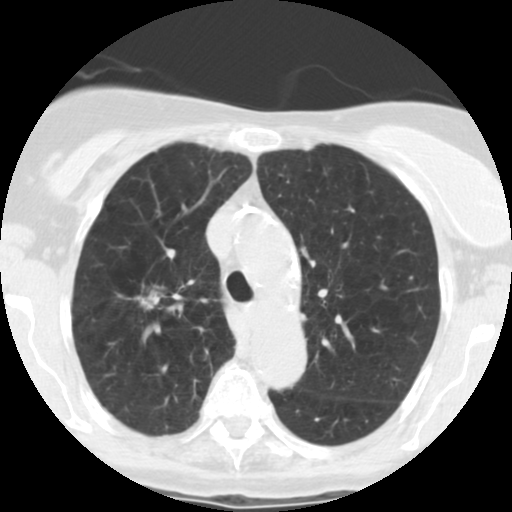
Axial slice from a low-dose chest CT screening exam, first (baseline) screen, lung window (W 1500 / L -600 HU), 2.5 mm slice thickness, slice 181 of 246 in the series. Female participant, aged 67 years at enrolment.
• Lesion marked by an expert reader, box from (x=114, y=277) to (x=177, y=319) px.
• The screening reader recorded 6 non-calcified nodules or masses ≥4 mm on this exam (right upper lobe, right middle lobe, left lower lobe, right middle lobe, left lower lobe, left lower lobe); which of them this box marks is not recorded.
• Lung cancer was diagnosed 15 days after this screen: adenocarcinoma, NOS, right upper lobe, moderately differentiated (G2), stage IA (AJCC 6th edition), 14 mm at pathology.